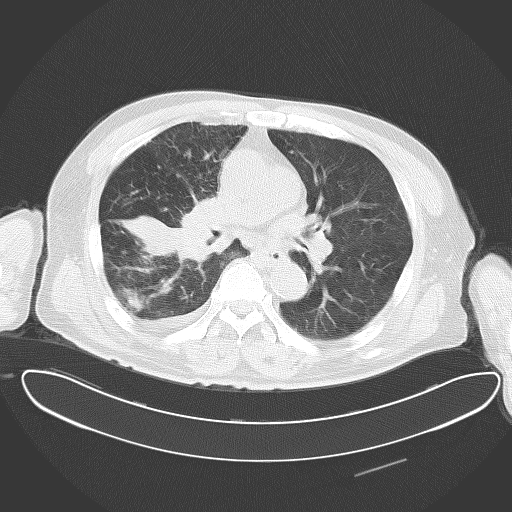
Chest CT, one axial slice; position 32 of 62 along the scan axis; 120 kVp; lung window (W 1500 / L -600 HU); 512 × 512 image matrix, field of view 427 × 427 mm. Patient: male, 78 years. Case-level facts recorded for this patient, not image findings: clinical TNM (as recorded): T2 N1 M1.
Structures marked on this image (rectangle marked by the reading radiologist):
- lung tumour (recorded histology: adenocarcinoma): bounding box <112,179,236,279> (left, top, right, bottom; pixels)